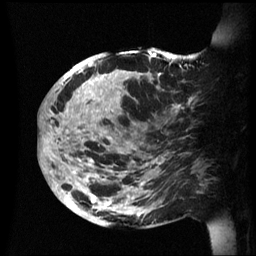
Breast MRI (dynamic contrast-enhanced), one sagittal slice. Slice 25 of 60 in the series (ordered by position). Dynamic contrast-enhanced series, image 2 of 3 at this slice position (ordered by acquisition). 1.5 T. TE 4.2 ms, TR 8.4 ms. 2.4 mm slice thickness. 256 × 256 image matrix, field of view 230 × 230 mm. Patient: female, 48 years.
Structures marked on this image (semi-automatic segmentation, software-assisted and operator-edited):
- analysis volume of interest (the breast-tissue region the enhancement analysis was run in; not a lesion): box from (x=42, y=47) to (x=202, y=228) px
- tumour enhancement mask (voxels above the 70 % enhancement threshold inside the analysis volume of interest): (x=42, y=51)–(x=185, y=224)